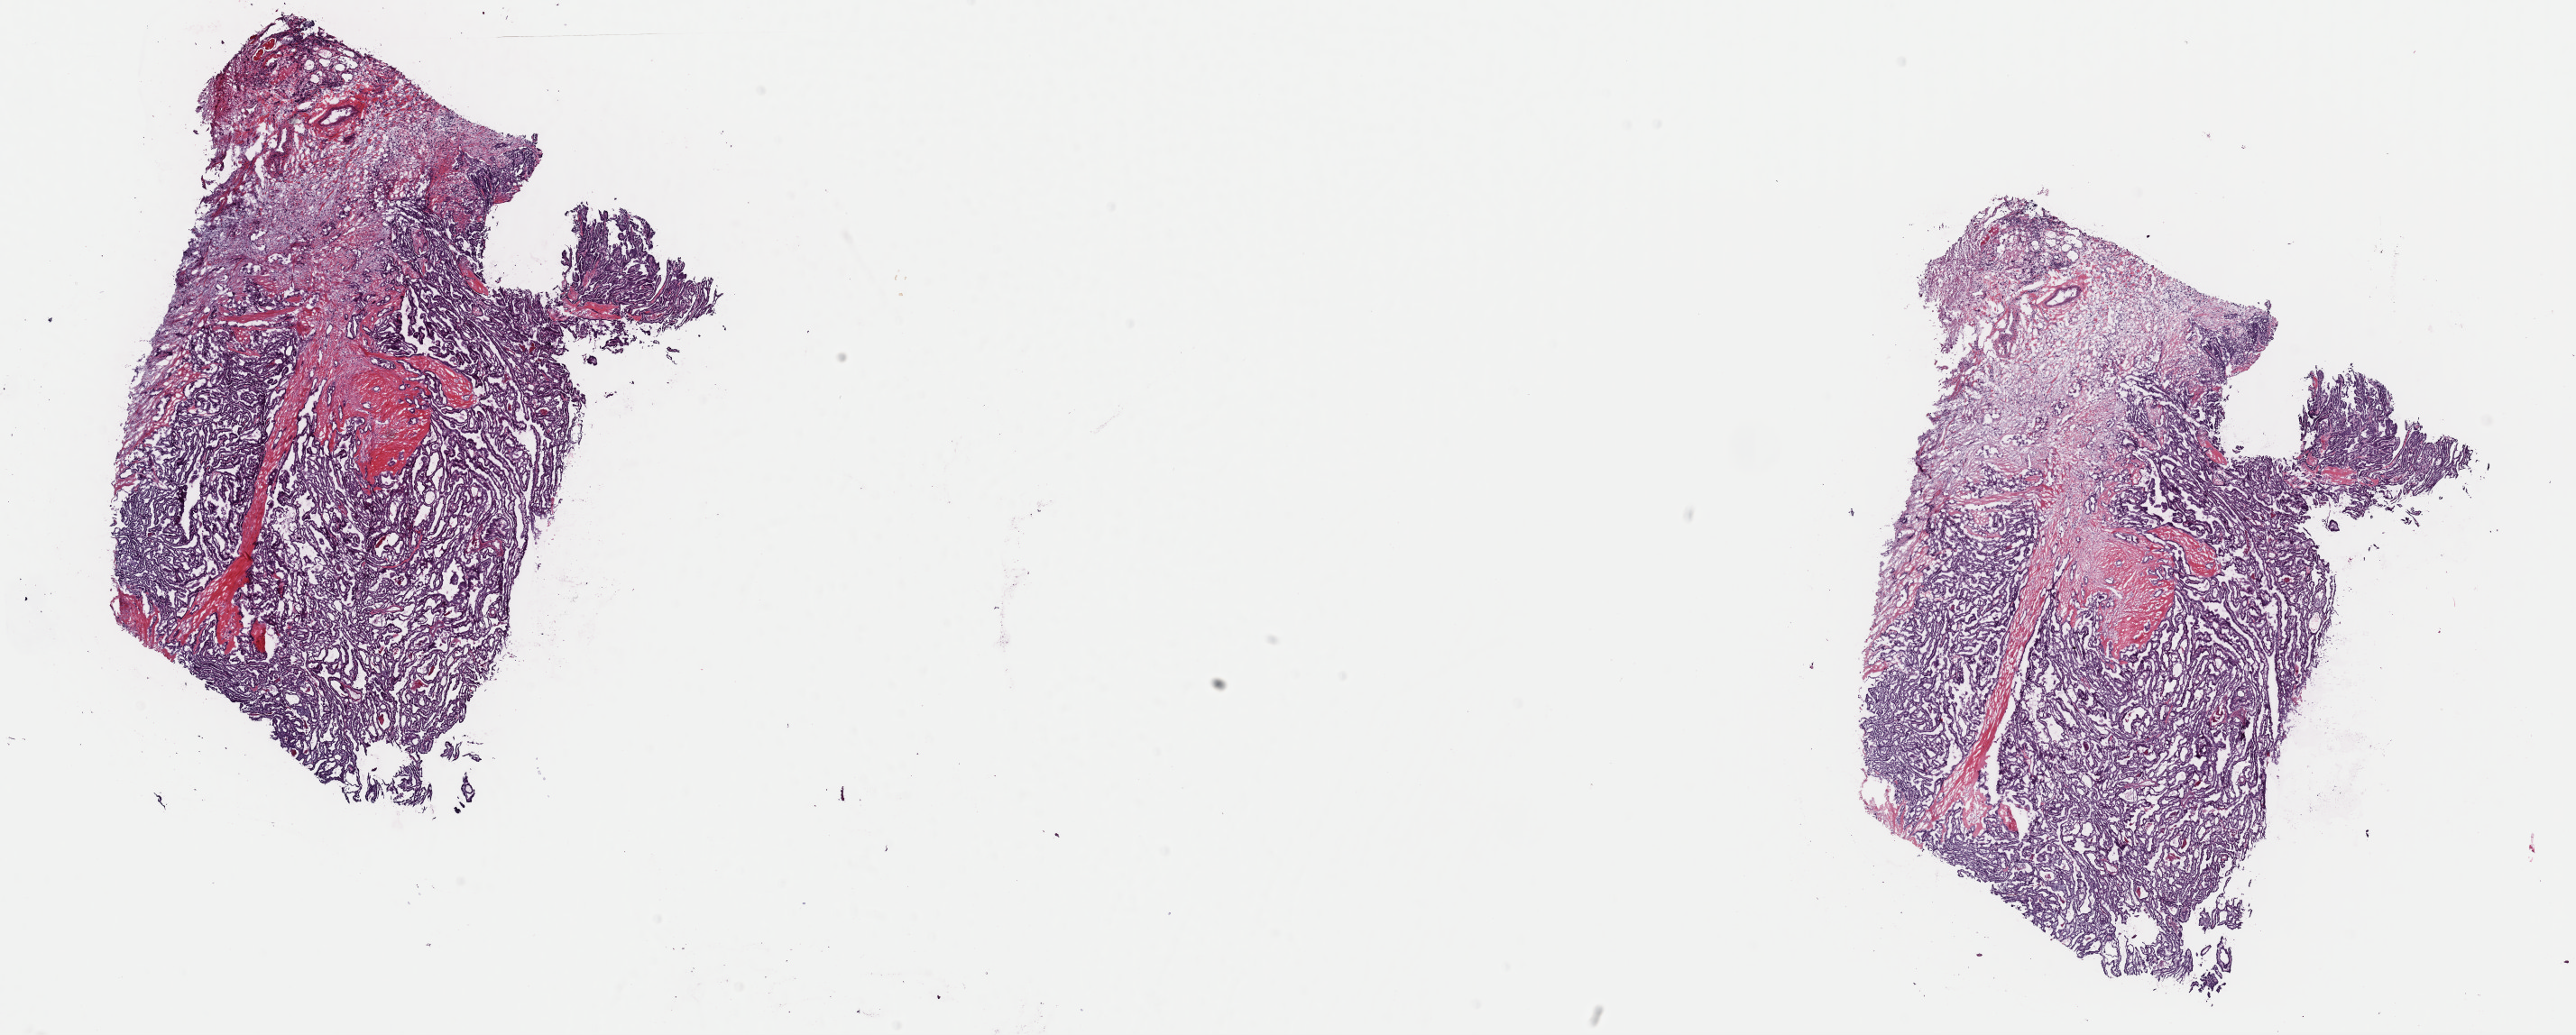
Digitized H&E-stained tissue section (whole slide) — low-resolution overview of the scanned area, about 22.6 x 9.1 mm (from a 40x scan); frozen section; primary tumour sample from the thyroid. Female, age 38 years at initial diagnosis. Composition of this section per pathologist review: tumour cells 80%, tumour nuclei 80%, normal cells 0%, stromal cells 20%, necrosis 0%. Inflammatory infiltration, as recorded: lymphocyte infiltration 4%, monocyte infiltration 1%, neutrophil infiltration 2%.
Lymph nodes positive (case pathology): 2 of 2 examined. Histologic diagnosis: Papillary adenocarcinoma, NOS (thyroid gland). TNM: T2 N1a M0. AJCC pathologic stage: I.